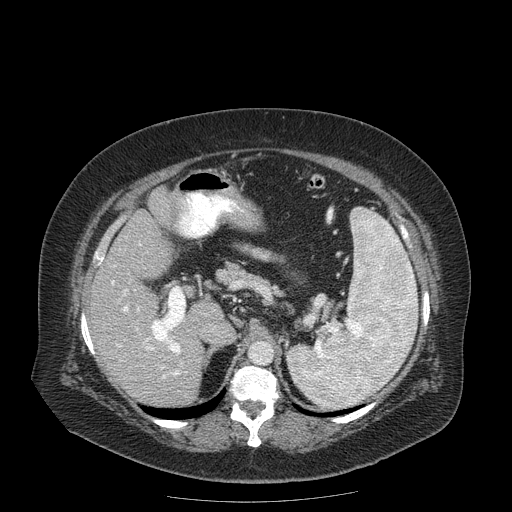
Contrast-enhanced abdominal CT (liver protocol), one axial slice. Position 107 of 204 along the scan axis. Reconstruction kernel STANDARD. Soft-tissue window (W 400 / L 40 HU). 512 × 512 image matrix. From the clinical record (not read from this slice): diagnosis: hepatocellular carcinoma (patient treated with transarterial chemoembolisation; whether this scan precedes or follows treatment is not stated here); TNM stage (as recorded): Stage-IIIB; Child-Pugh class: A; tumour differentiation: well differentiated; tumour nodularity: uninodular.
Annotated regions visible in this slice (semi-automatically segmented with operator editing):
- liver parenchyma outside the tumour (the mass and vessels are separate outlines, so this box may not span the whole liver): bounding box (x1, y1, x2, y2) in pixels: (88, 188, 222, 406)
- liver vessels: (111, 281, 184, 379)